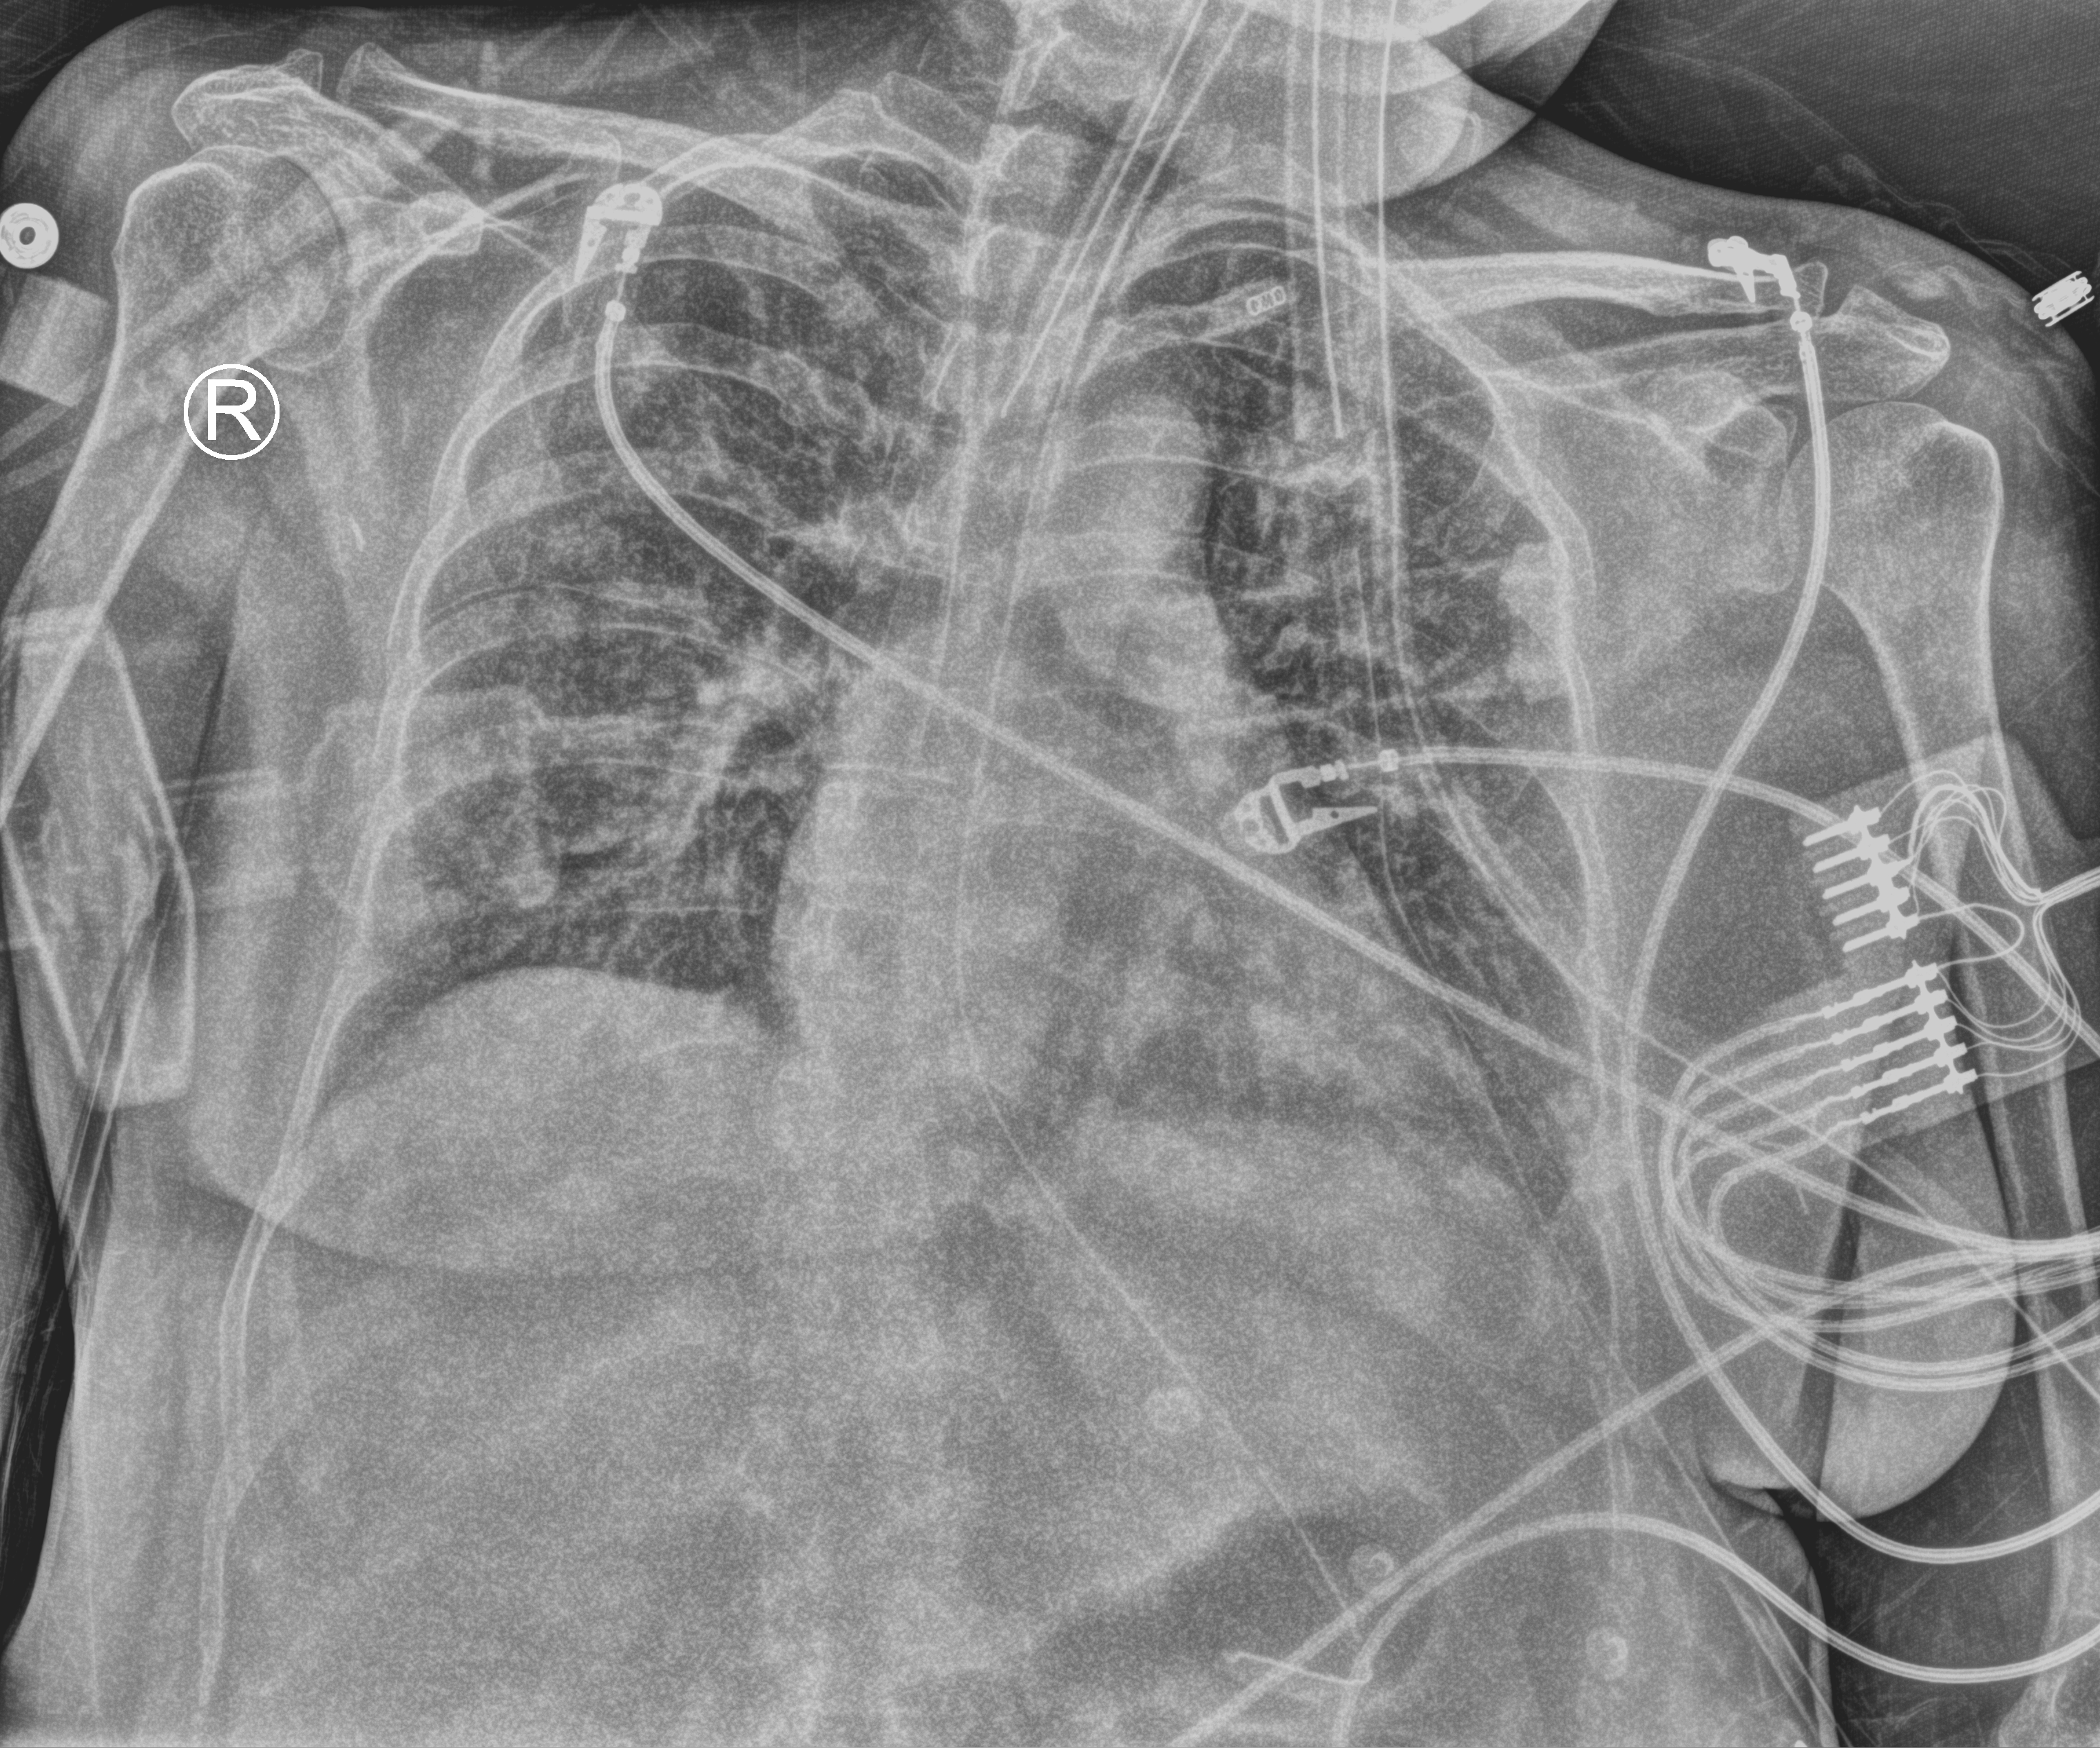
Portable chest radiograph; anteroposterior (AP) projection. Patient hospitalised with COVID-19; female, aged 18–59 years.
From the hospital-stay record, not from the radiograph (when in the stay this image was taken is not recorded): smoking status (admission record): never; mechanically ventilated during this hospital stay: yes; admitted to intensive care during this hospital stay: no.